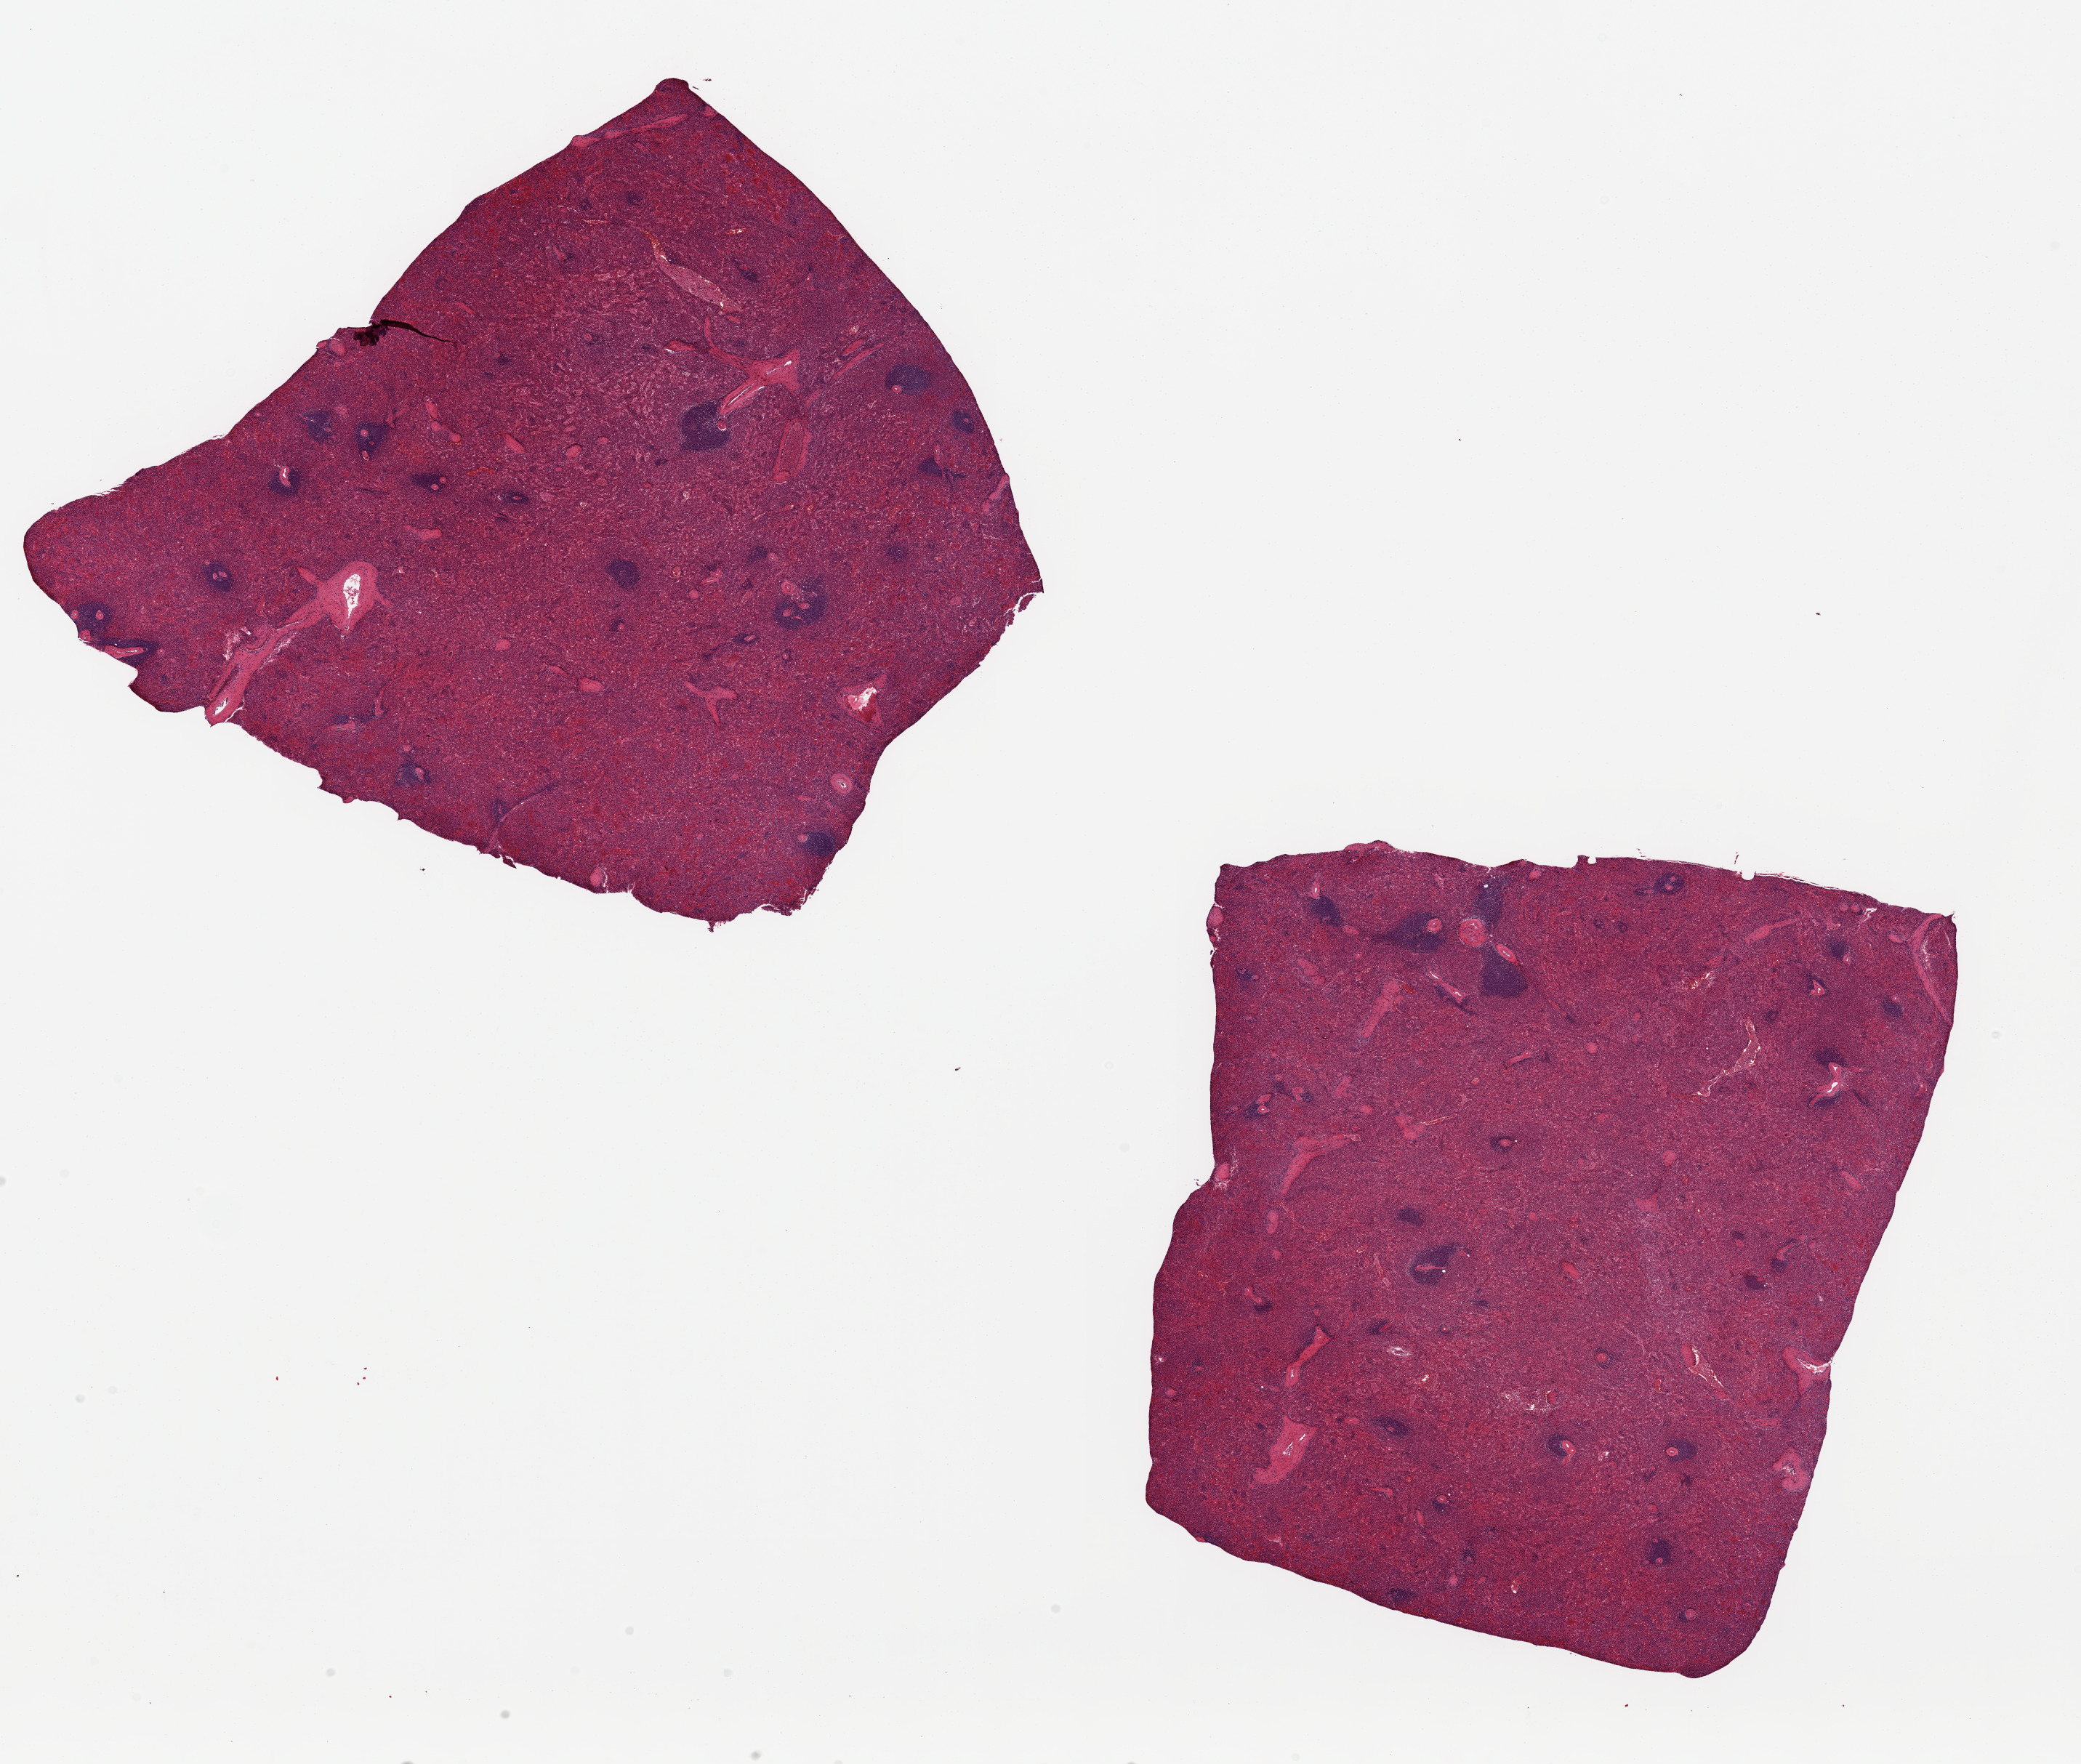
Whole-slide image, H&E stain, brightfield — low-resolution overview of the scanned area, about 22.6 x 19.2 mm (from a 20x scan), PAXgene-fixed, paraffin-embedded tissue, target tissue: spleen, tissue donor sample. Donor sex: male.
Pathologist's review note for this sample: 2 ~8x8mm pieces.